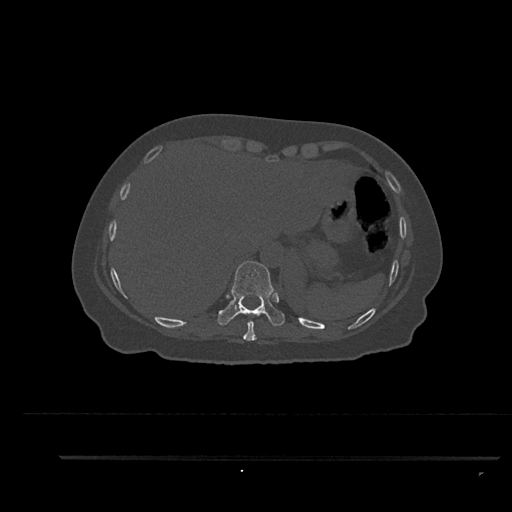
CT including the spine, one axial slice; position 375 of 797 along the scan axis; bone window (W 1800 / L 400 HU); 512 × 512 image matrix. Patient: female, 44 years. Case-level facts recorded for this patient, not image findings: primary cancer: renal; vertebrae with lytic lesions (as recorded): L1.
Annotated regions visible in this slice (semi-automatically segmented with operator editing):
- T10 vertebra: bounding box <217,260,285,326> (left, top, right, bottom; pixels)
- T9 vertebra: <243,321,257,341>